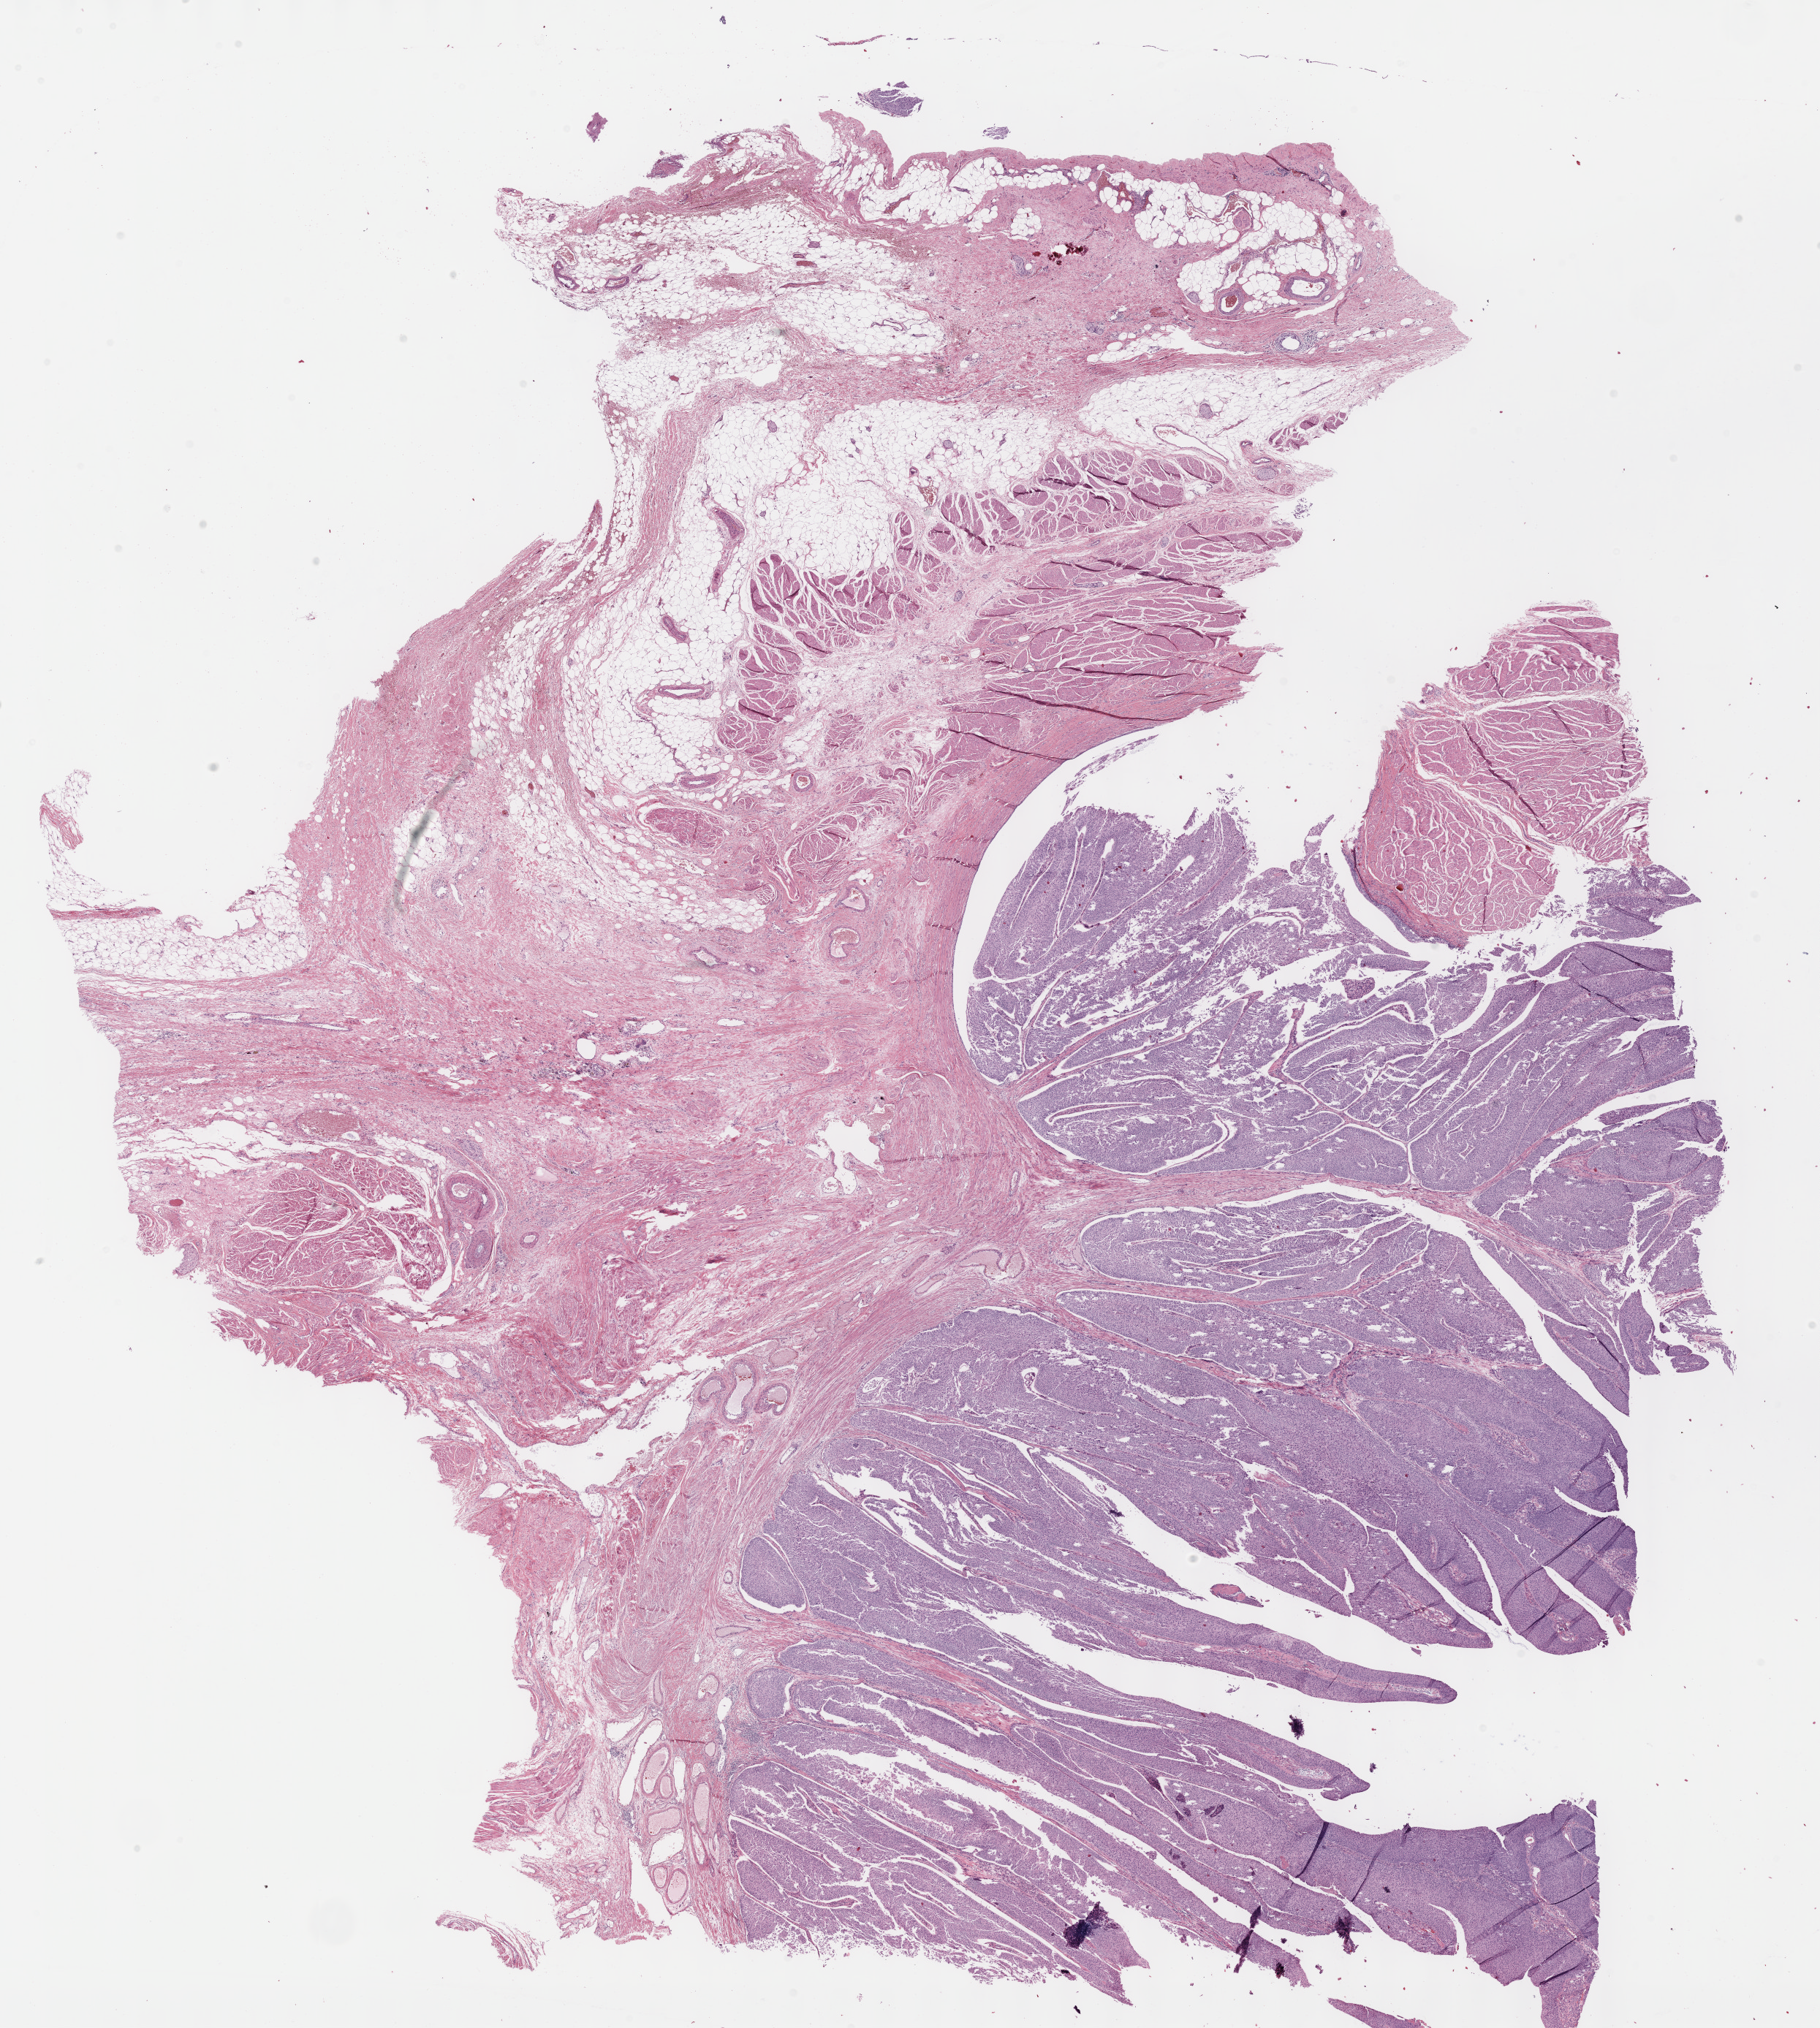
Whole-slide histology image, H&E, a low-resolution overview of the entire scanned area, about 20.1 x 22.4 mm (from a 40x scan); formalin-fixed paraffin-embedded (FFPE) diagnostic section; primary tumour sample from the bladder. Male, age 60 years at initial diagnosis.
Pathologic diagnosis: Papillary transitional cell carcinoma (lateral wall of bladder).